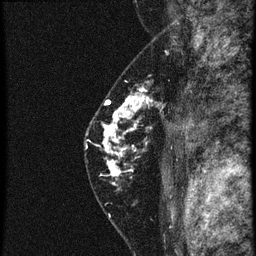
Breast MRI (dynamic contrast-enhanced), one sagittal slice. Position 41 of 60 along the scan axis. 4 images stored at this slice position (order not interpretable as contrast timing). 1.5 T. TE 4.2 ms, TR 20.4 ms. 1.5 mm slice thickness. 256 × 256 image matrix. Female patient, age 46 years. From the clinical record (not read from this slice): setting: breast cancer imaged before/during neoadjuvant chemotherapy; receptor status: triple-negative.
Outlined on this slice (semi-automatically segmented with operator editing):
- analysis volume of interest (the breast-tissue region the enhancement analysis was run in; not a lesion): box from (x=88, y=82) to (x=181, y=185) px
- tumour enhancement mask (voxels above the 90 % enhancement threshold inside the analysis volume of interest): (x=102, y=90)–(x=153, y=185)